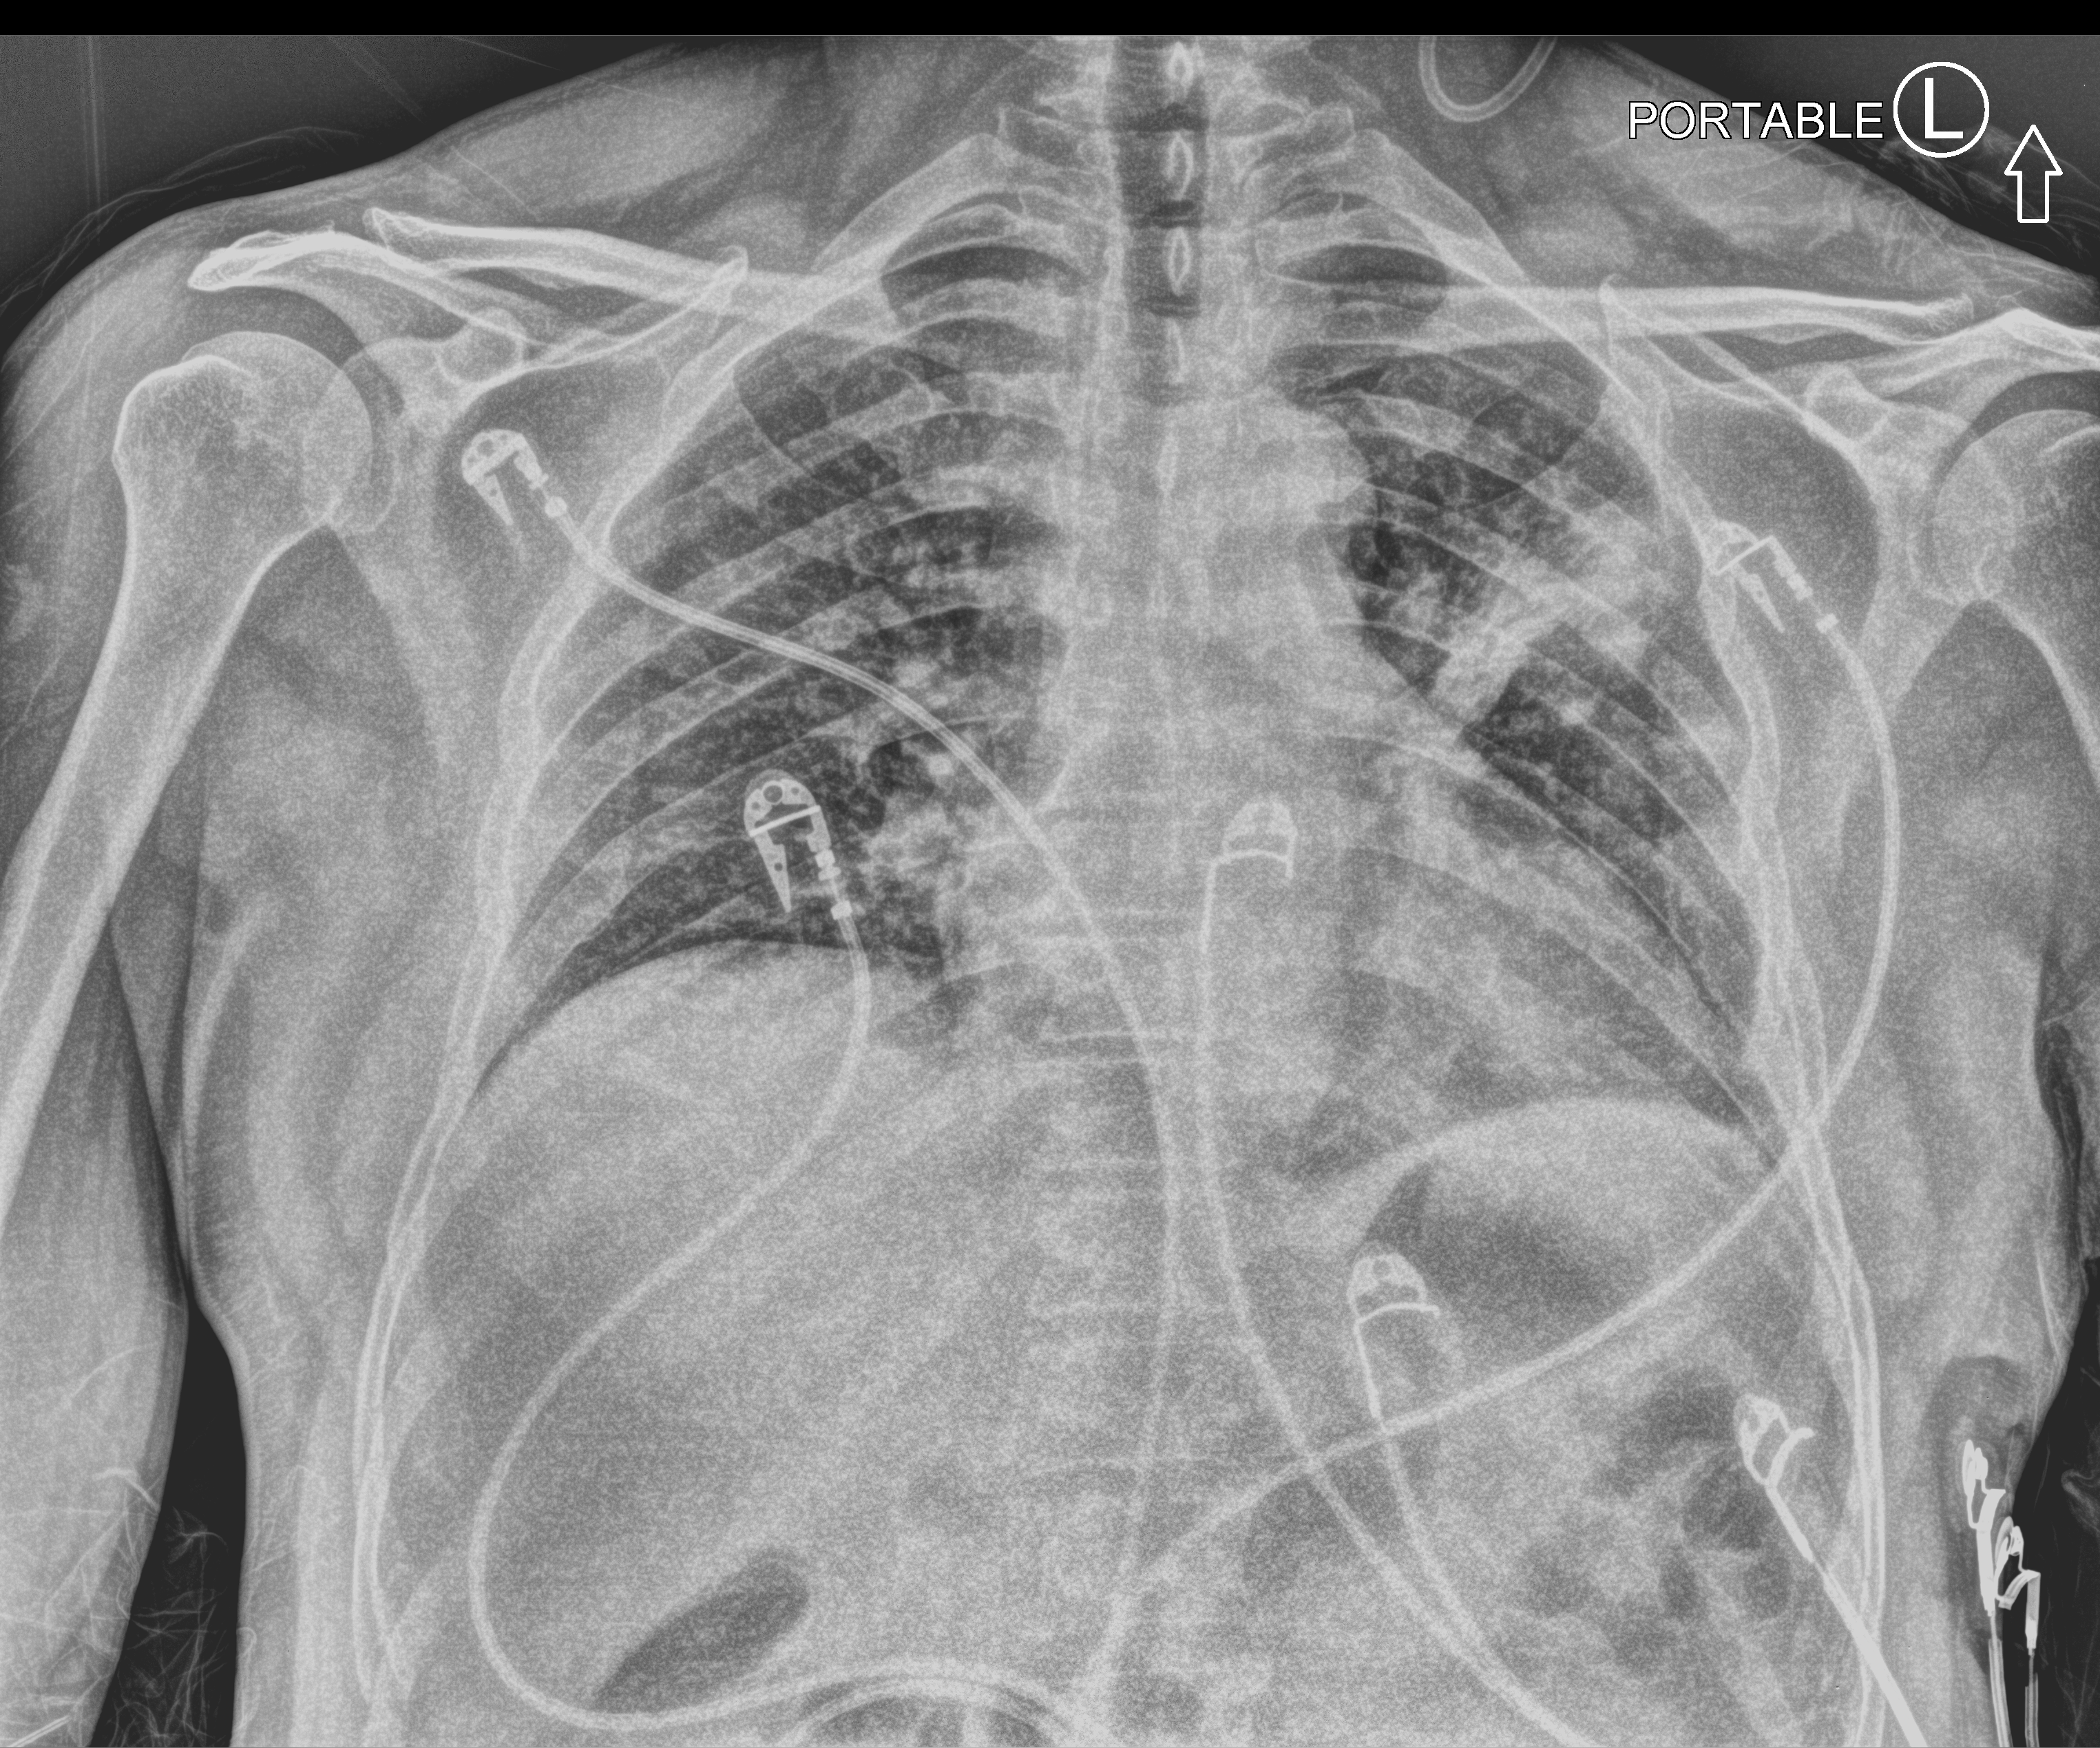
Bedside chest radiograph (computed radiography); anteroposterior (AP) projection. Male patient hospitalised with COVID-19, age 18–59 years.
Admission-level facts for this patient (not findings on this image; timing relative to this image not recorded):
- length of hospital stay: 14 days
- COPD (admission record): no
- mechanically ventilated during this hospital stay: yes